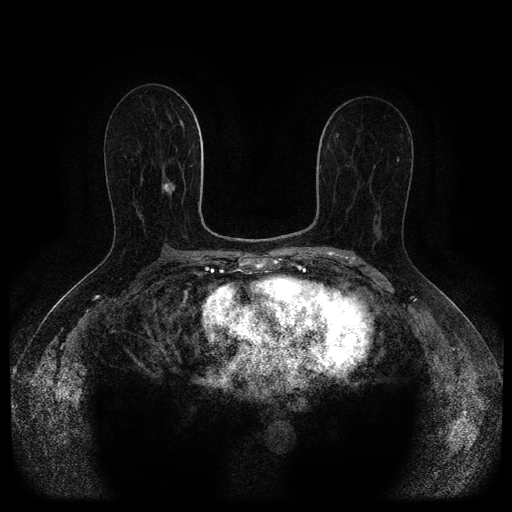
Breast MRI (dynamic contrast-enhanced, multi-phase), one axial slice. Slice 56 of 116 in the series (ordered by position). Dynamic contrast-enhanced series, time point 2 of 5 at this slice position (early post-contrast). 1.5 T. TE 2.7 ms, TR 5.4 ms. 2 mm slice thickness. 512 × 512 image matrix. Patient: female, 71 years.
Outlined on this slice (semi-automatic segmentation, software-assisted and operator-edited):
- breast lesion (labelled 'tumour' in the annotation; benign lesions carry a separate 'benign' label): bounding box <162,182,175,195> (left, top, right, bottom; pixels)